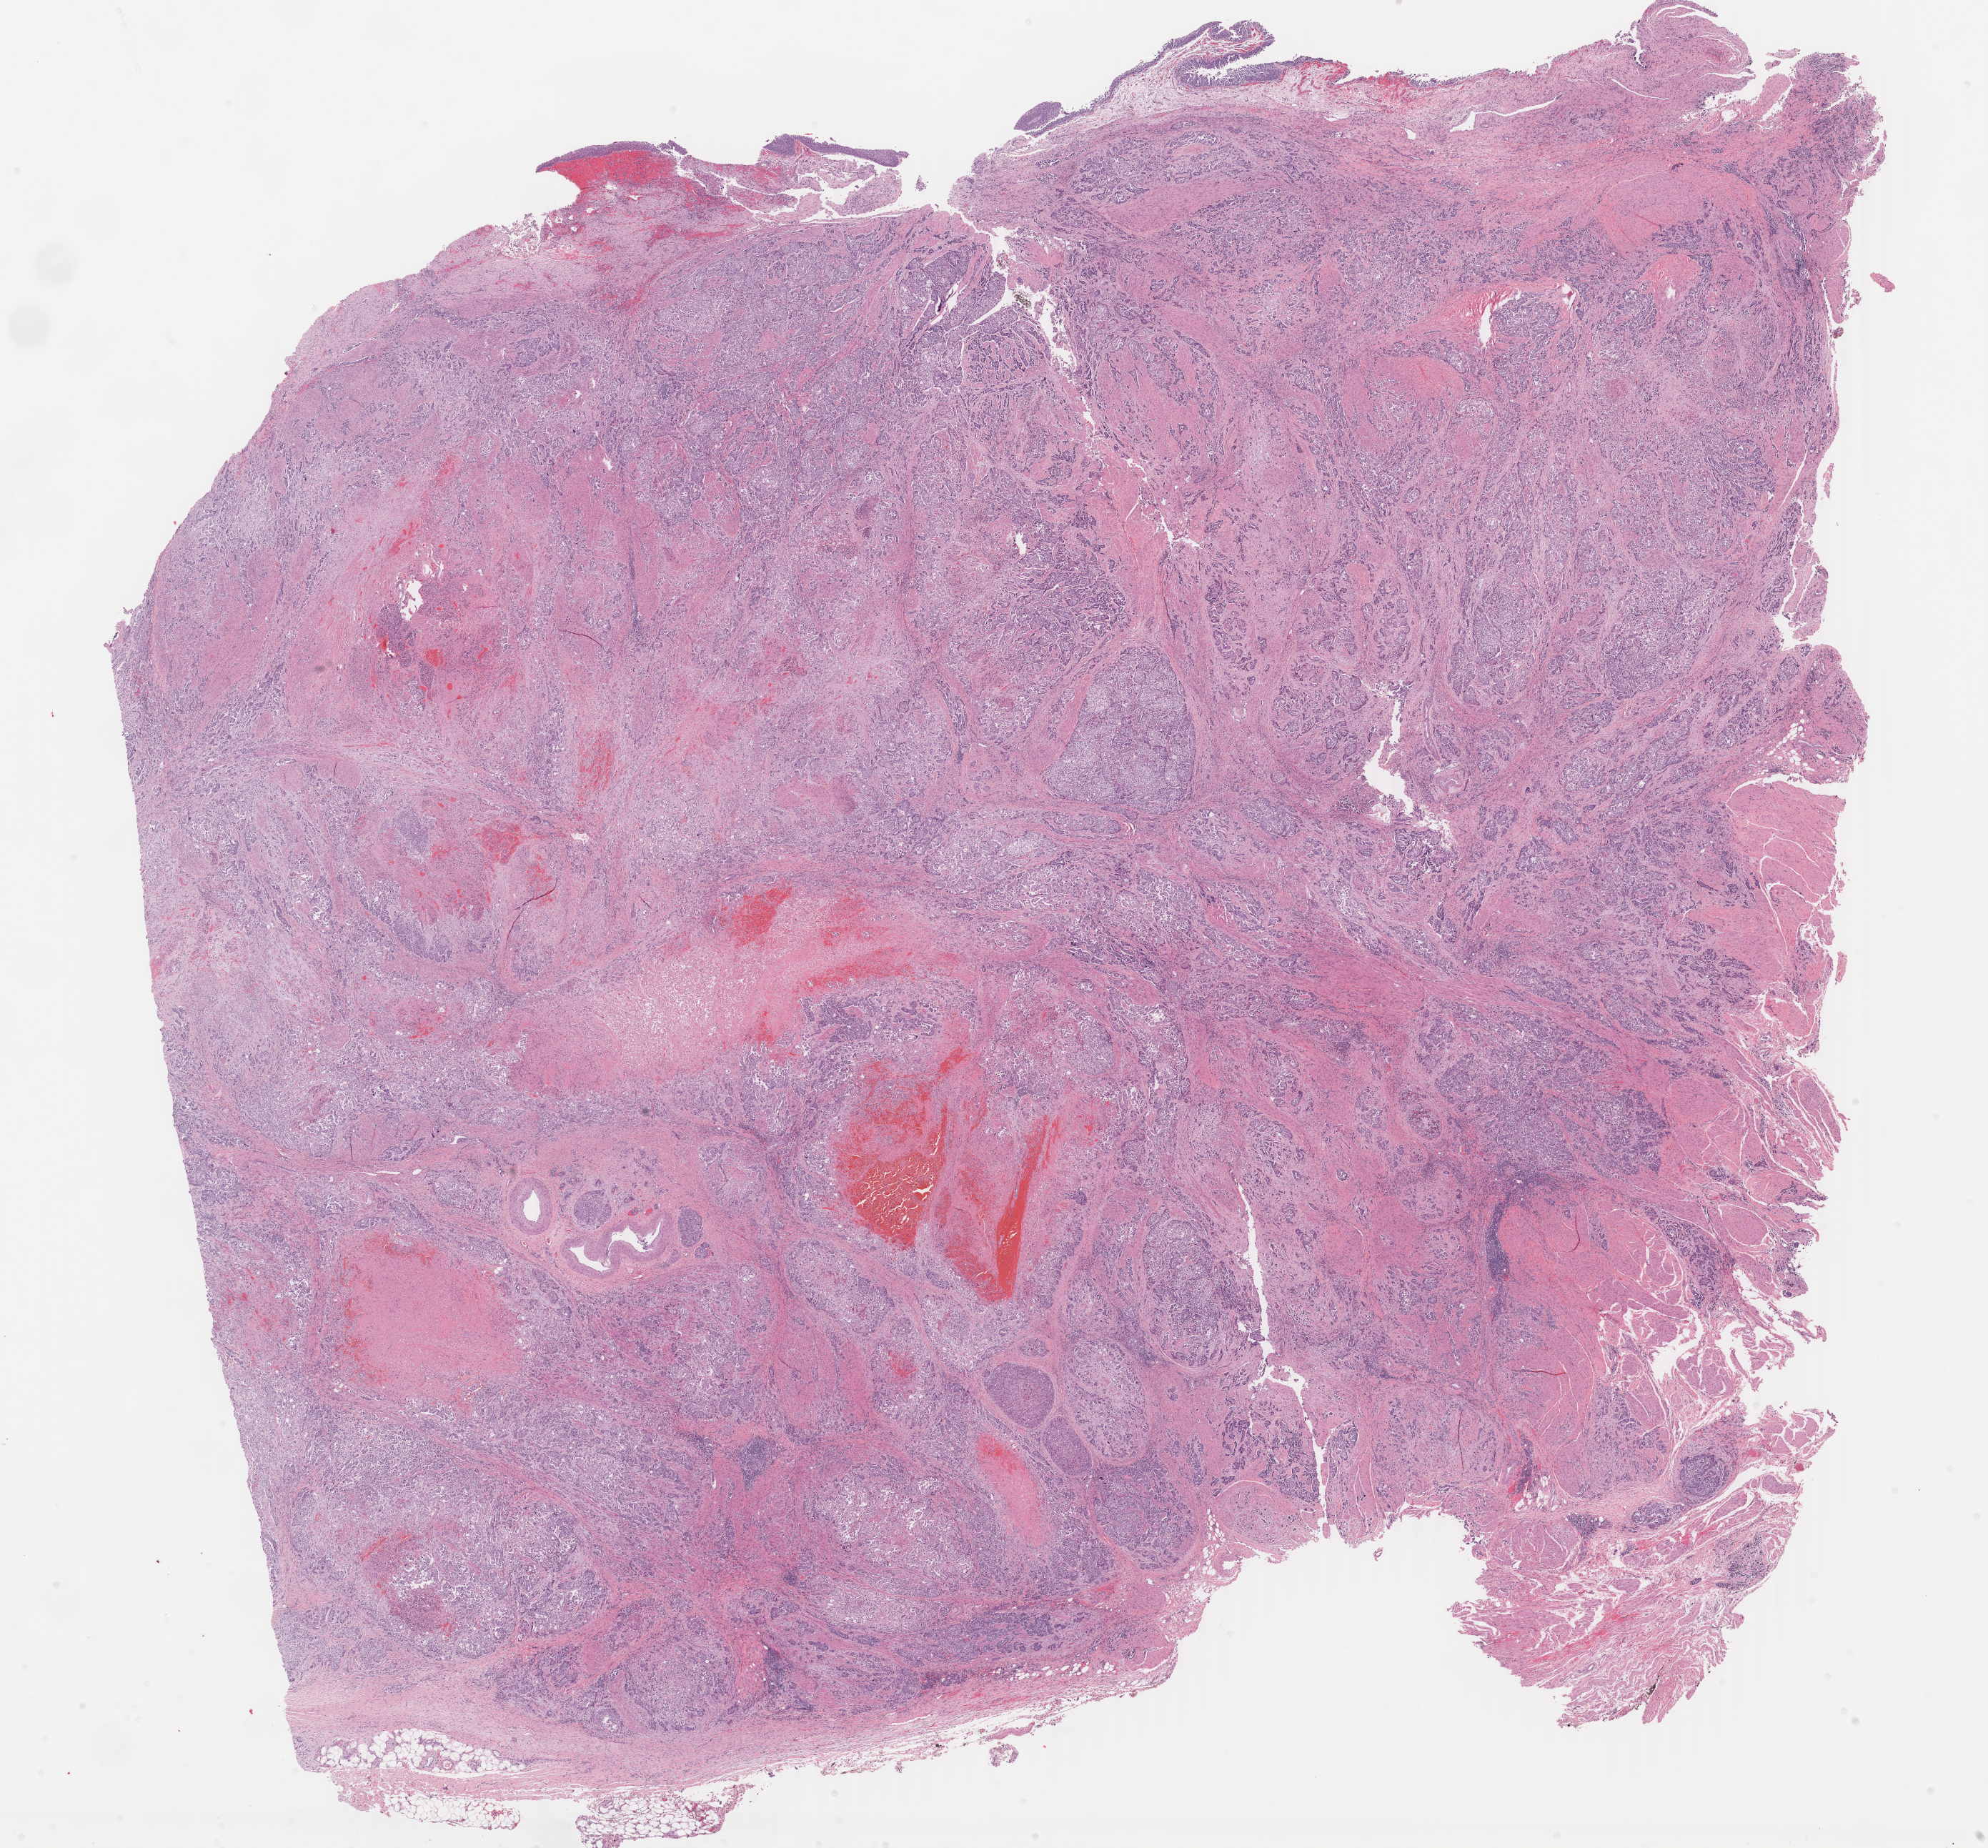
Digitized H&E tissue section (whole slide), shown as a low-resolution overview of the whole scanned area (about 22.1 x 20.6 mm, from a 40x scan); formalin-fixed paraffin-embedded (FFPE) diagnostic section; bladder, primary tumour sample. Male, age 66 years at initial diagnosis. Histologic grade: high grade.
TNM: T4 N3 MX. Diagnosis: Transitional cell carcinoma (trigone of bladder). AJCC pathologic stage: IV (7th edition). Lymph nodes positive (case pathology): 22 of 28 examined.